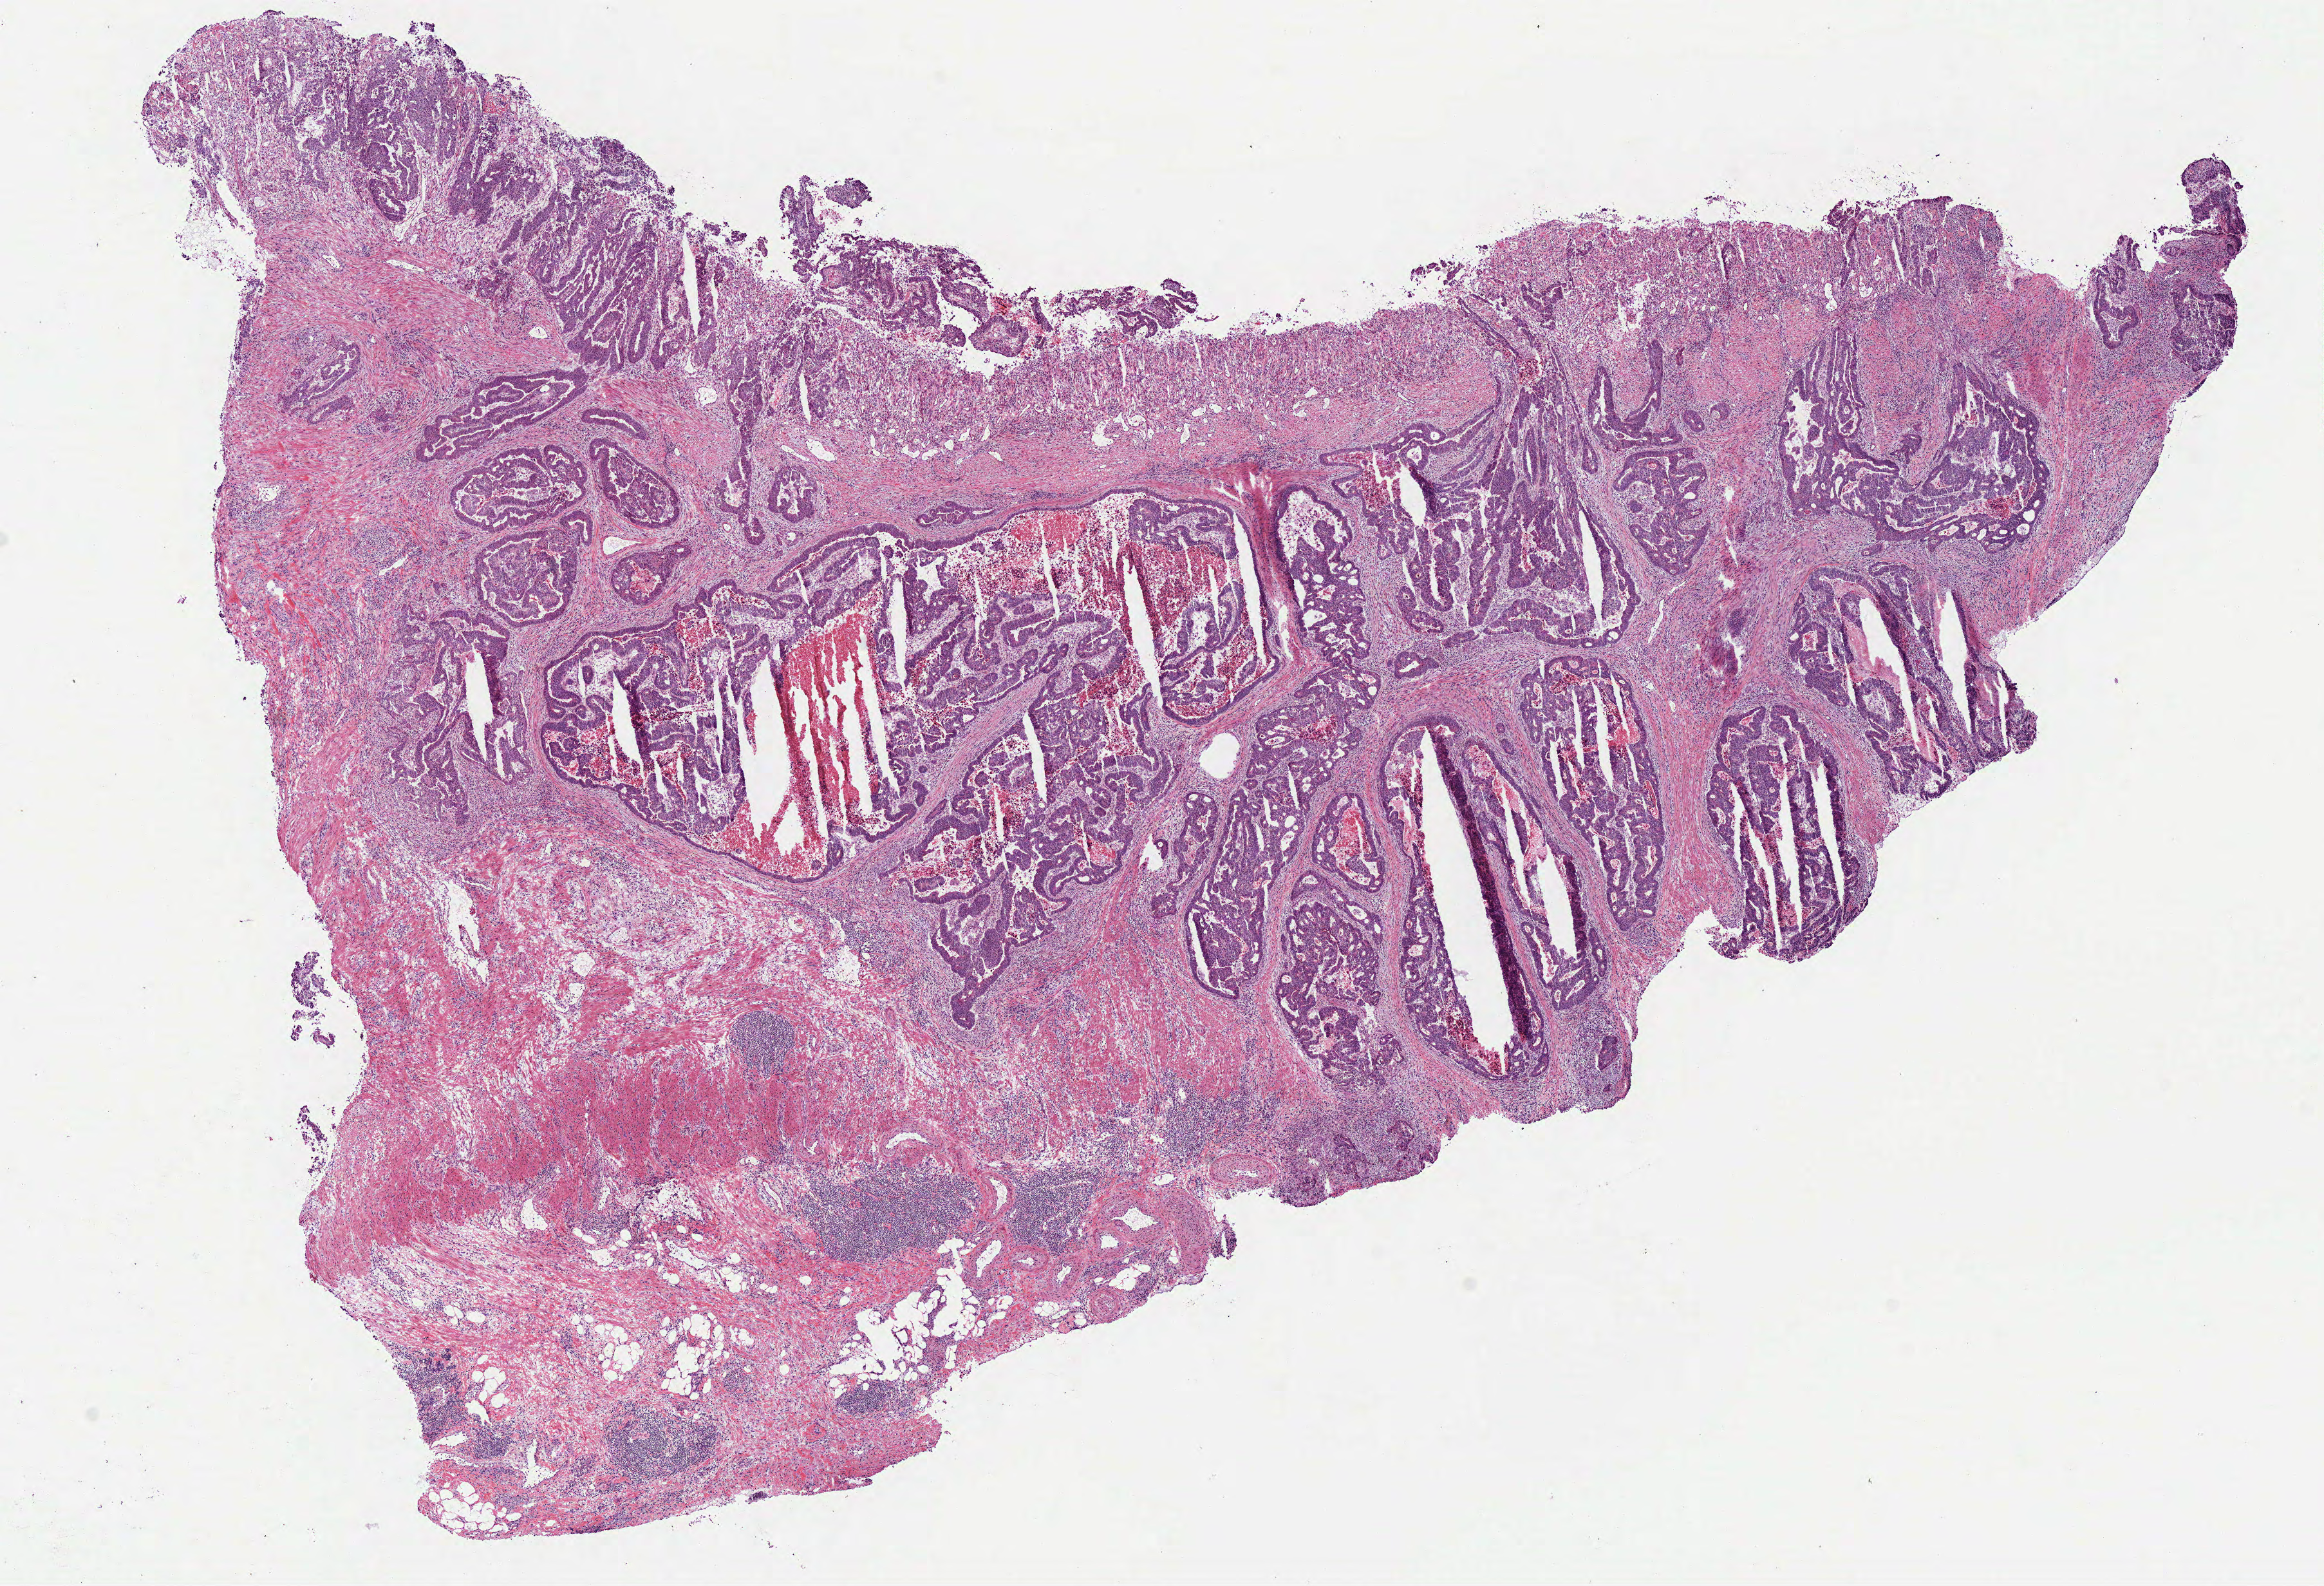
Whole-slide histology image, H&E — whole scanned area (about 14.2 x 9.7 mm, acquisition: 40x scan) shown as a low-resolution overview, frozen section from the bottom of the tissue portion, sample: primary tumour, colon. Patient: male, age at initial diagnosis 67 years. Composition of this section per pathologist review: tumour cells 80%, tumour nuclei 80%, normal cells 0%, stromal cells 15%, necrosis 5%.
- lymph nodes positive (case pathology): 0 of 19 examined
- pathologic diagnosis: Adenocarcinoma, NOS (cecum)
- AJCC pathologic stage: IIA (7th edition)